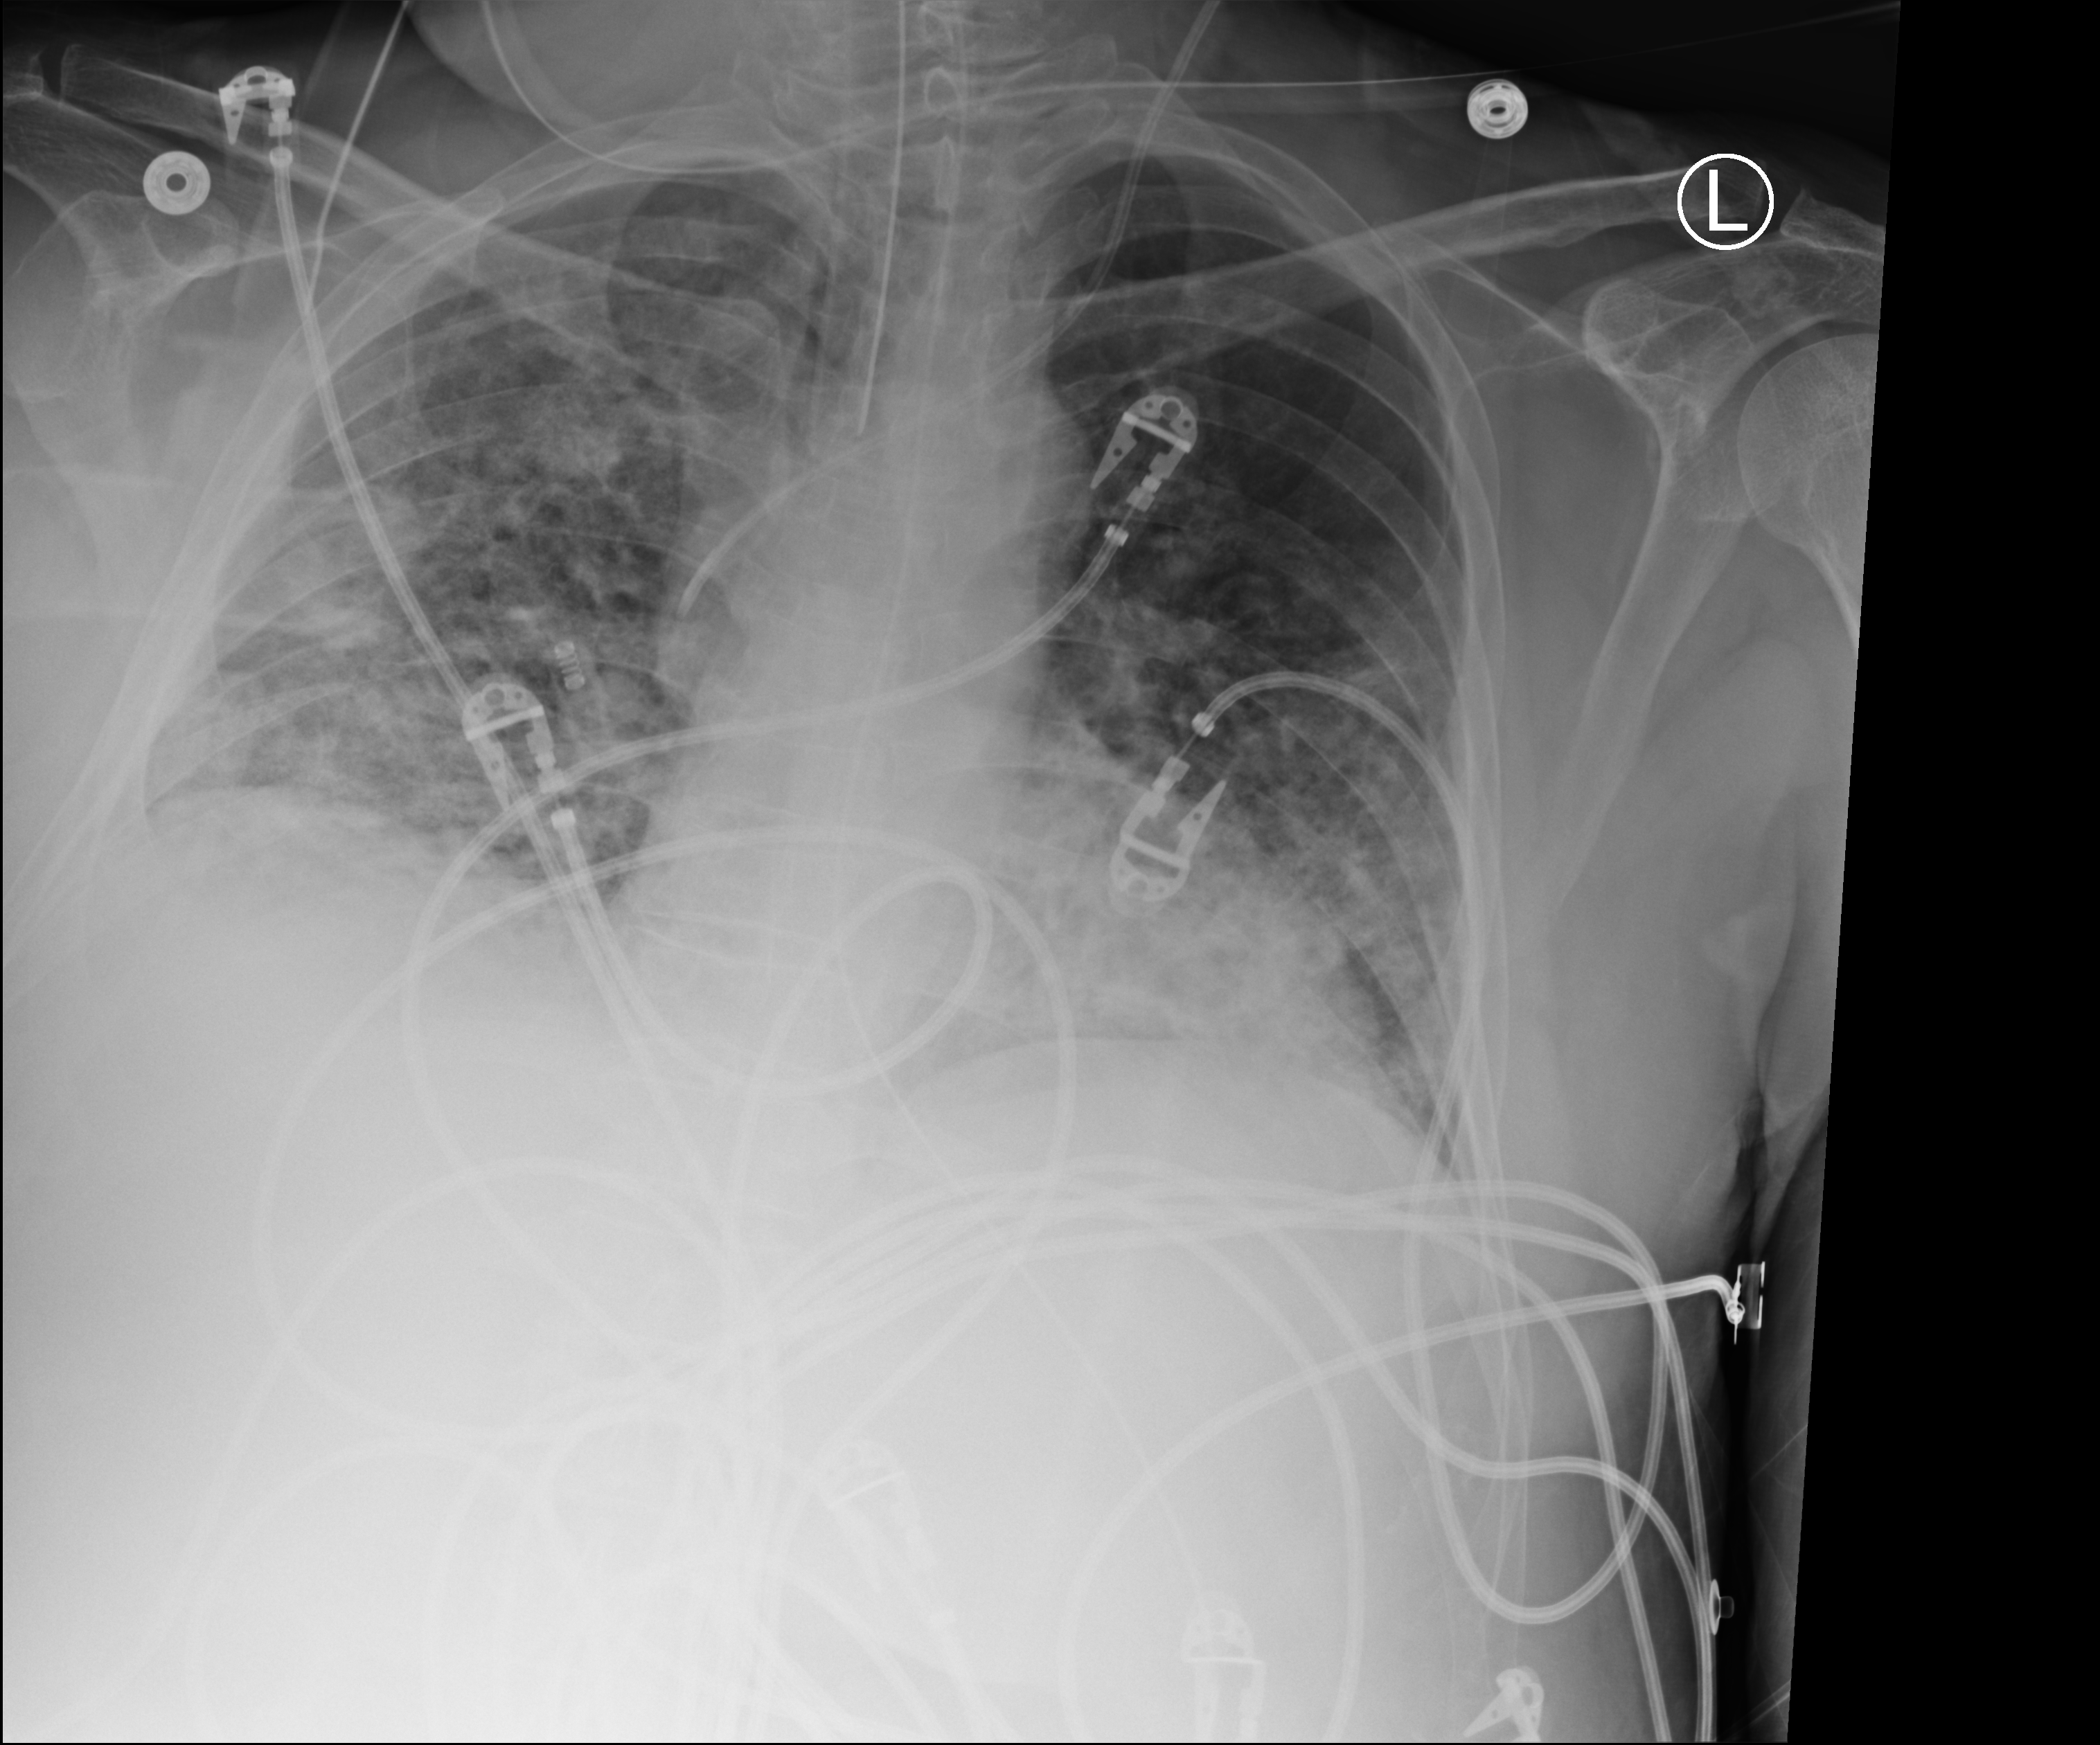
Portable chest radiograph; anteroposterior (AP) projection. Male patient hospitalised with COVID-19, age 60–74 years.
Admission-level facts for this patient (not findings on this image; timing relative to this image not recorded): COPD (admission record): no; admitted to intensive care during this hospital stay: yes; hypertension (admission record): no.